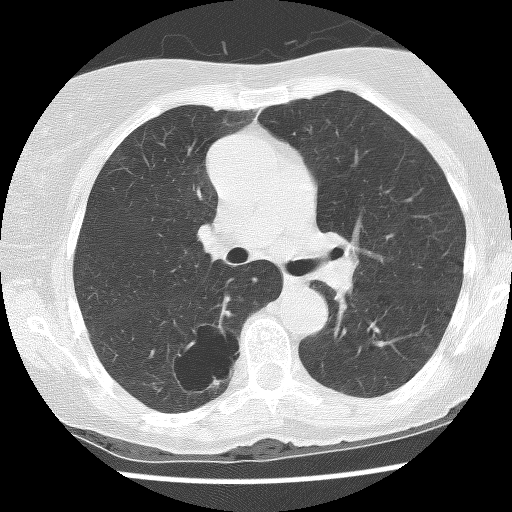
Low-dose screening chest CT, axial slice. Baseline screening round. Lung window (W 1500 / L -600 HU). 2.5 mm slice thickness. 120 kVp. Female, age 69 years at enrolment.
Expert reader's lesion annotation, bounding box <159,320,247,395> (left, top, right, bottom; pixels). The screening reader recorded 2 non-calcified nodules or masses ≥4 mm on this exam (right lower lobe, right lower lobe); which of them this box marks is not recorded.